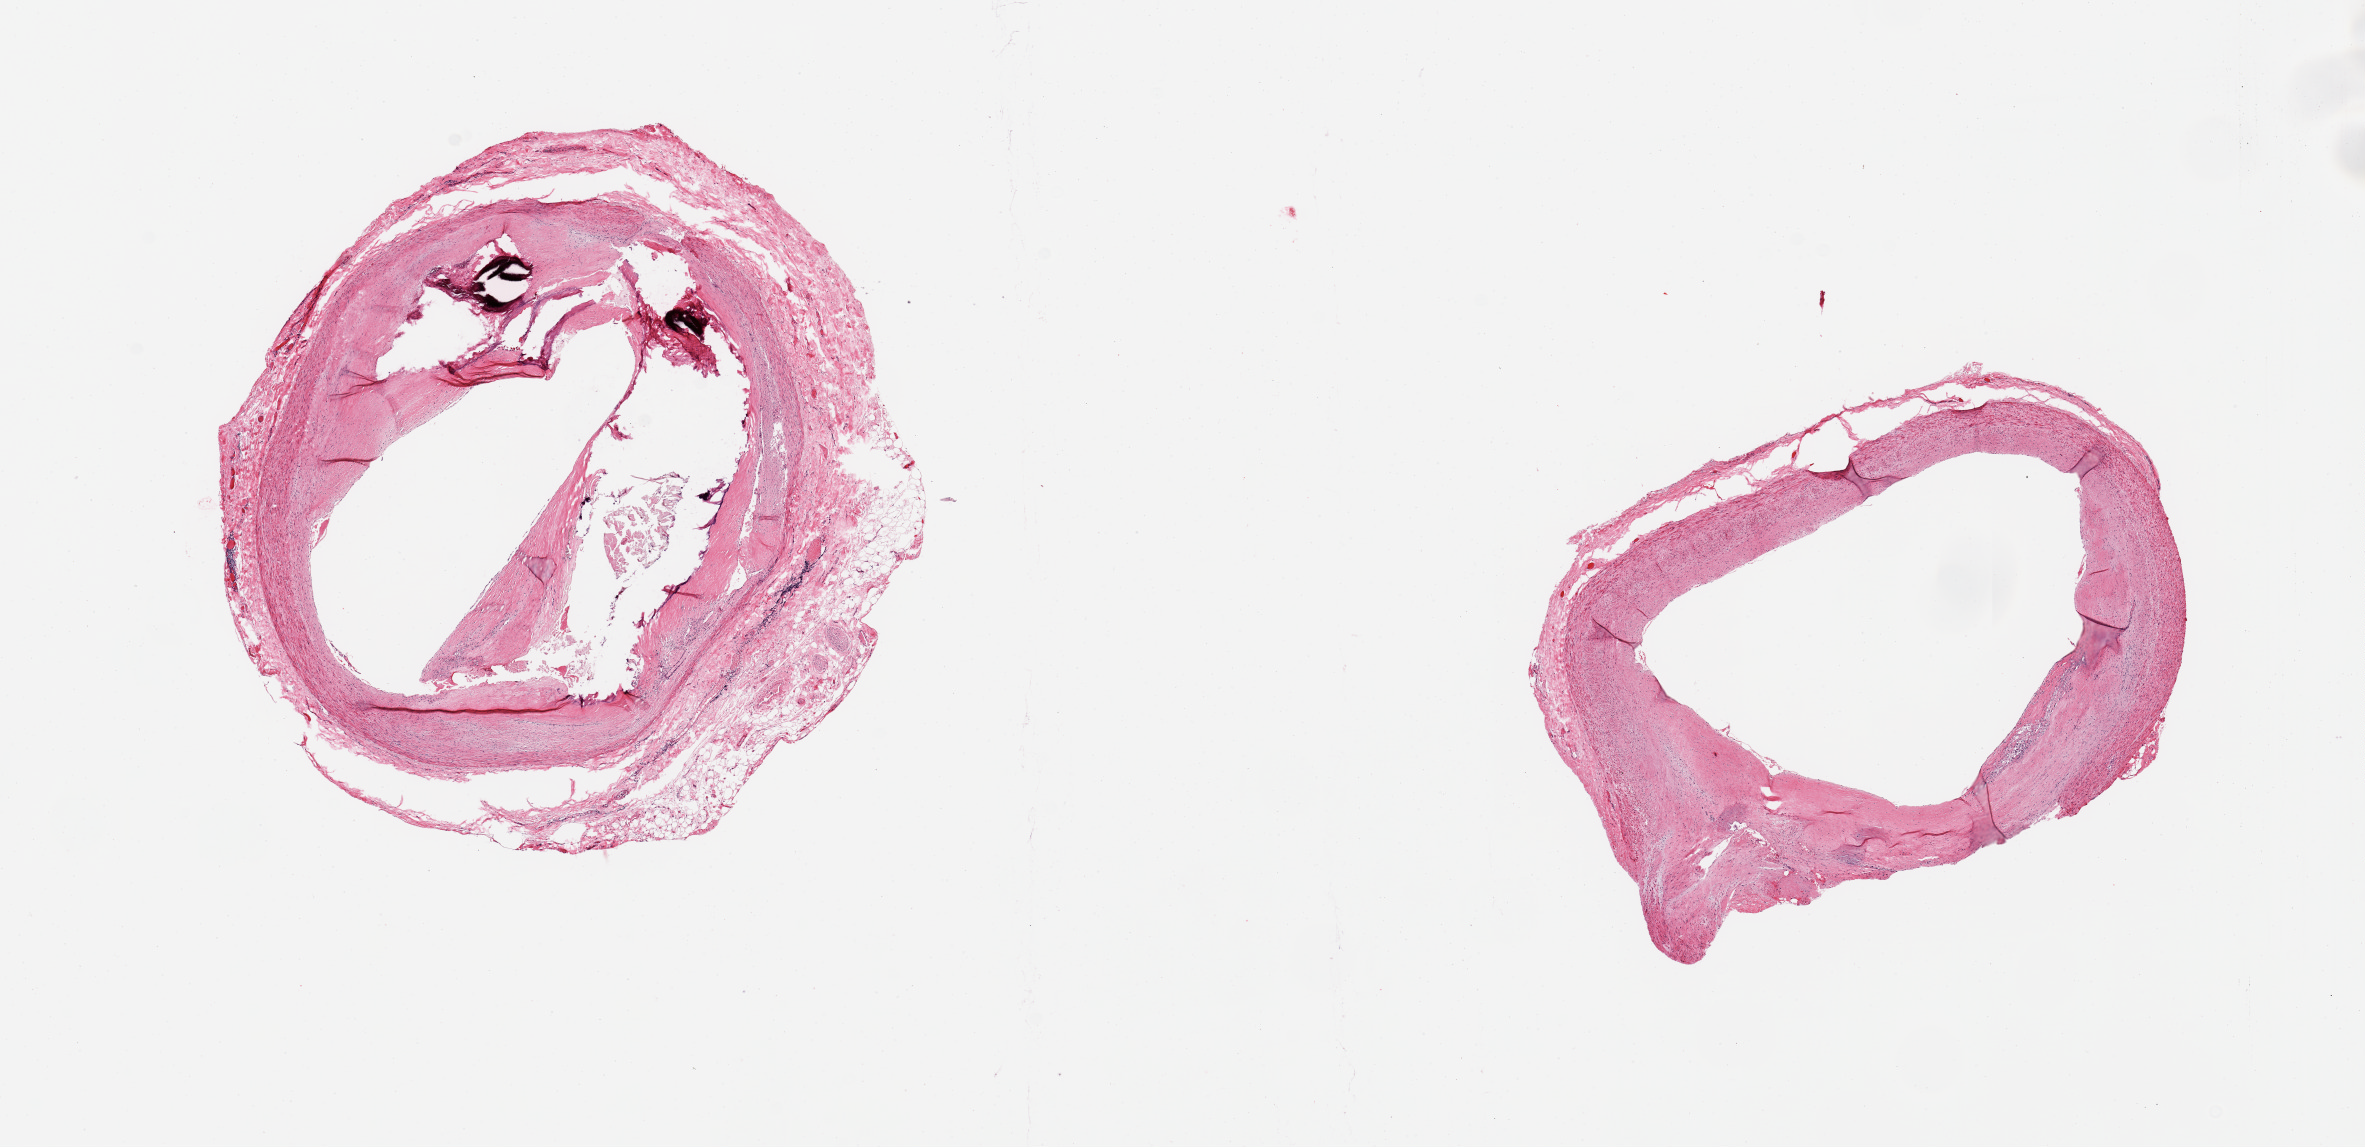
H&E whole-slide image — low-resolution overview of the scanned area, about 18.7 x 9.1 mm, PAXgene-fixed, paraffin-embedded tissue, target tissue: coronary artery, tissue donor sample. Donor: male.
Pathologist's review note for this sample: 2 pieces; heavily calcified atheromatous plaque in 1 piece; other piece appears atheromatous without calcium.